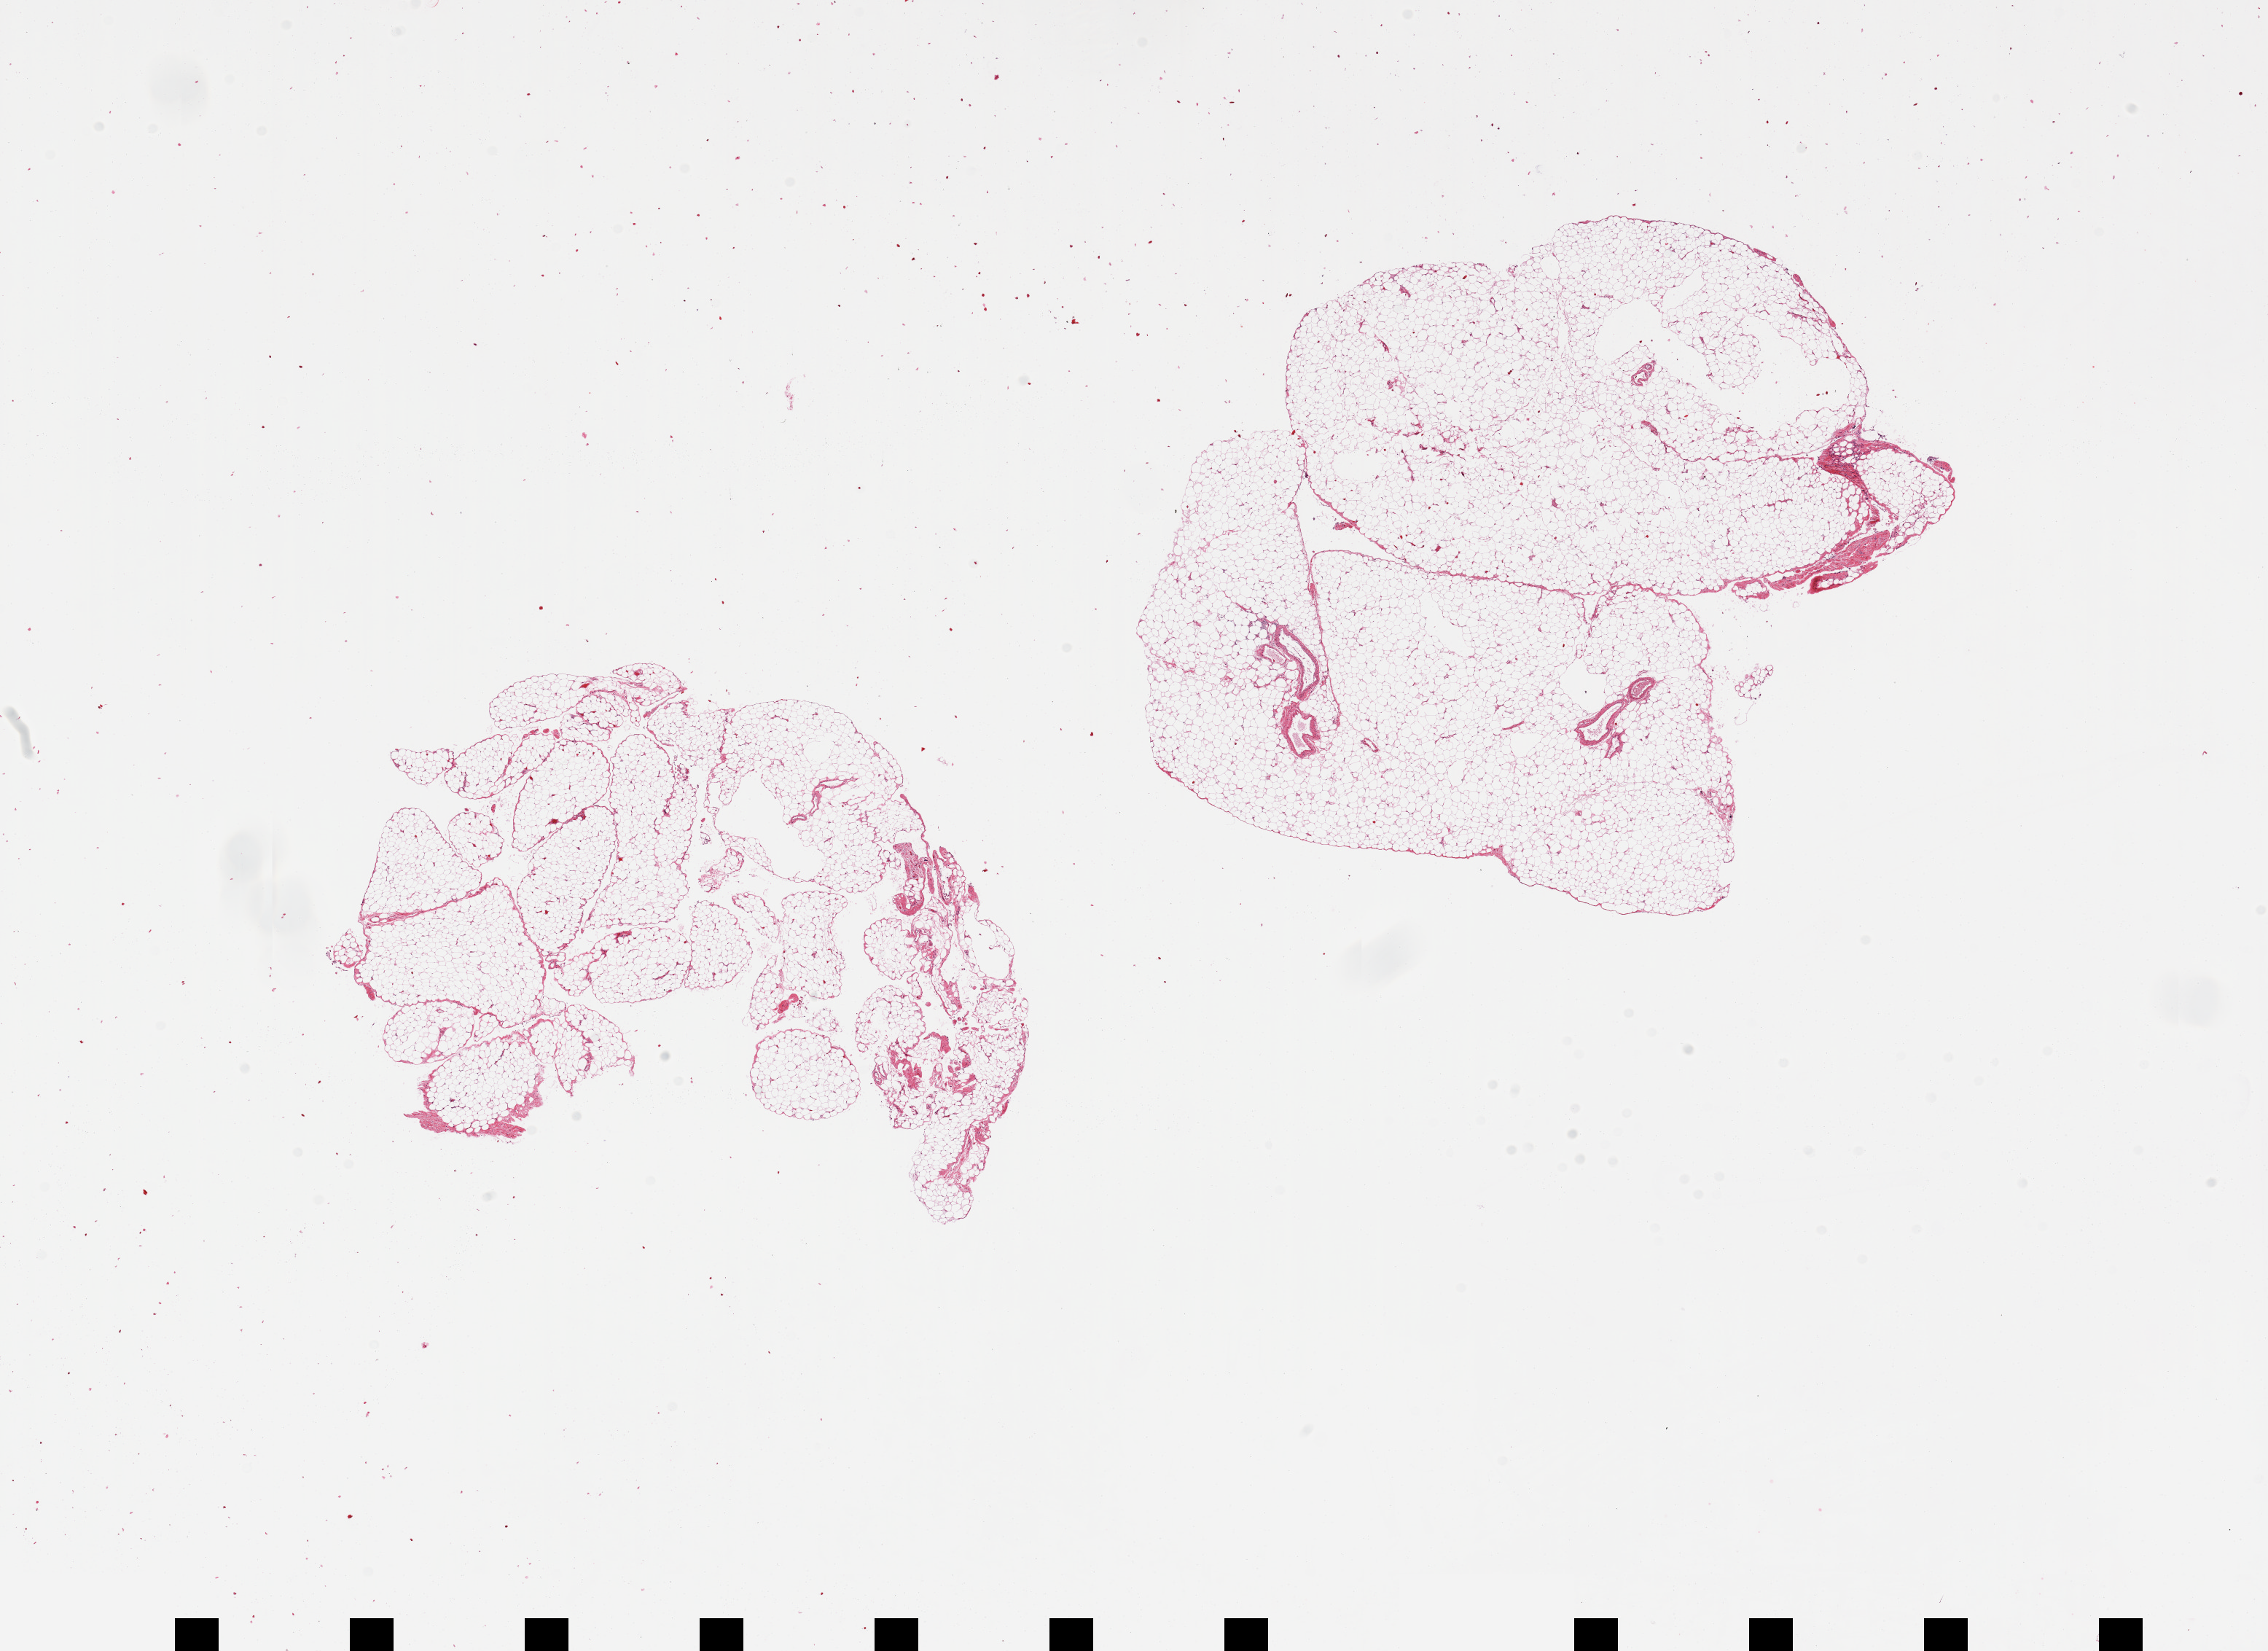
Whole-slide image, H&E stain, whole scanned area (about 24.6 x 17.9 mm, from a 20x scan) shown as a low-resolution overview. PAXgene-fixed paraffin-embedded (PFPE) section. Sampled site (target tissue): omentum. Donor tissue sample. Donor: female.
Review note (as recorded): 2 pieces.